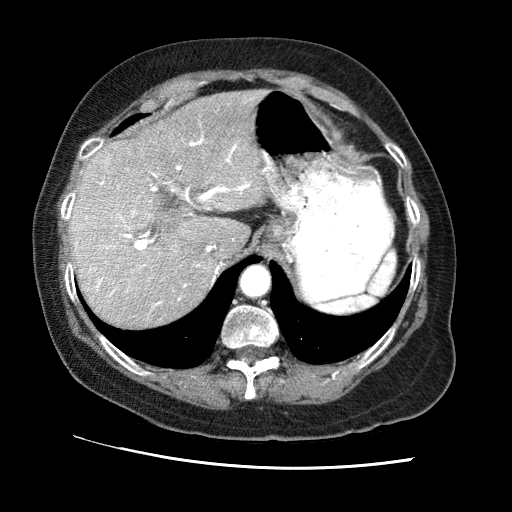
Contrast-enhanced abdominal CT (liver protocol), one axial slice; slice 48 of 65 in the series (ordered by position); reconstruction kernel STANDARD; 120 kVp; soft-tissue window (W 400 / L 40 HU); 512 × 512 image matrix. From the clinical record (not read from this slice): diagnosis: hepatocellular carcinoma (patient treated with transarterial chemoembolisation; whether this scan precedes or follows treatment is not stated here); TNM stage (as recorded): Stage-II; Child-Pugh class: A; tumour differentiation: no biopsy; tumour nodularity: multinodular.
Outlined on this slice (semi-automatically segmented with operator editing):
- liver parenchyma outside the tumour (the mass and vessels are separate outlines, so this box may not span the whole liver): box from (x=70, y=90) to (x=266, y=326) px
- liver vessels: (x=76, y=138)–(x=251, y=306)